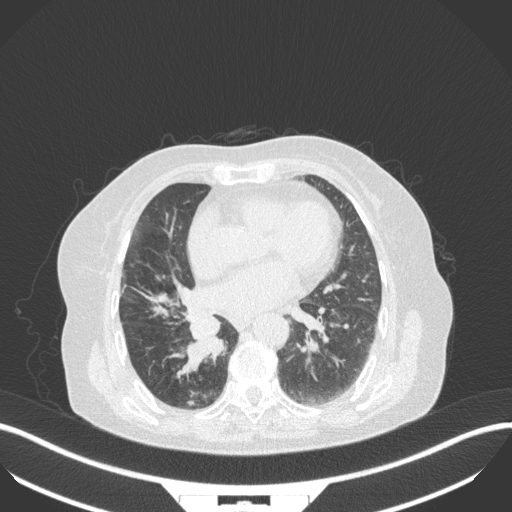
Chest CT, one axial slice; reconstruction kernel B31f; 120 kVp; lung window (W 1500 / L -600 HU); 1 mm slice thickness; 512 × 512 image matrix, field of view 400 × 400 mm. Patient: female, 75 years. From the clinical record (not read from this slice): clinical TNM (as recorded): T1b N0 M1a; histopathological grade: G1.
Structures marked on this image (bounding box drawn by a radiologist):
- lung tumour (recorded histology: squamous cell carcinoma): bounding box [x1, y1, x2, y2] px = [180, 309, 224, 375]